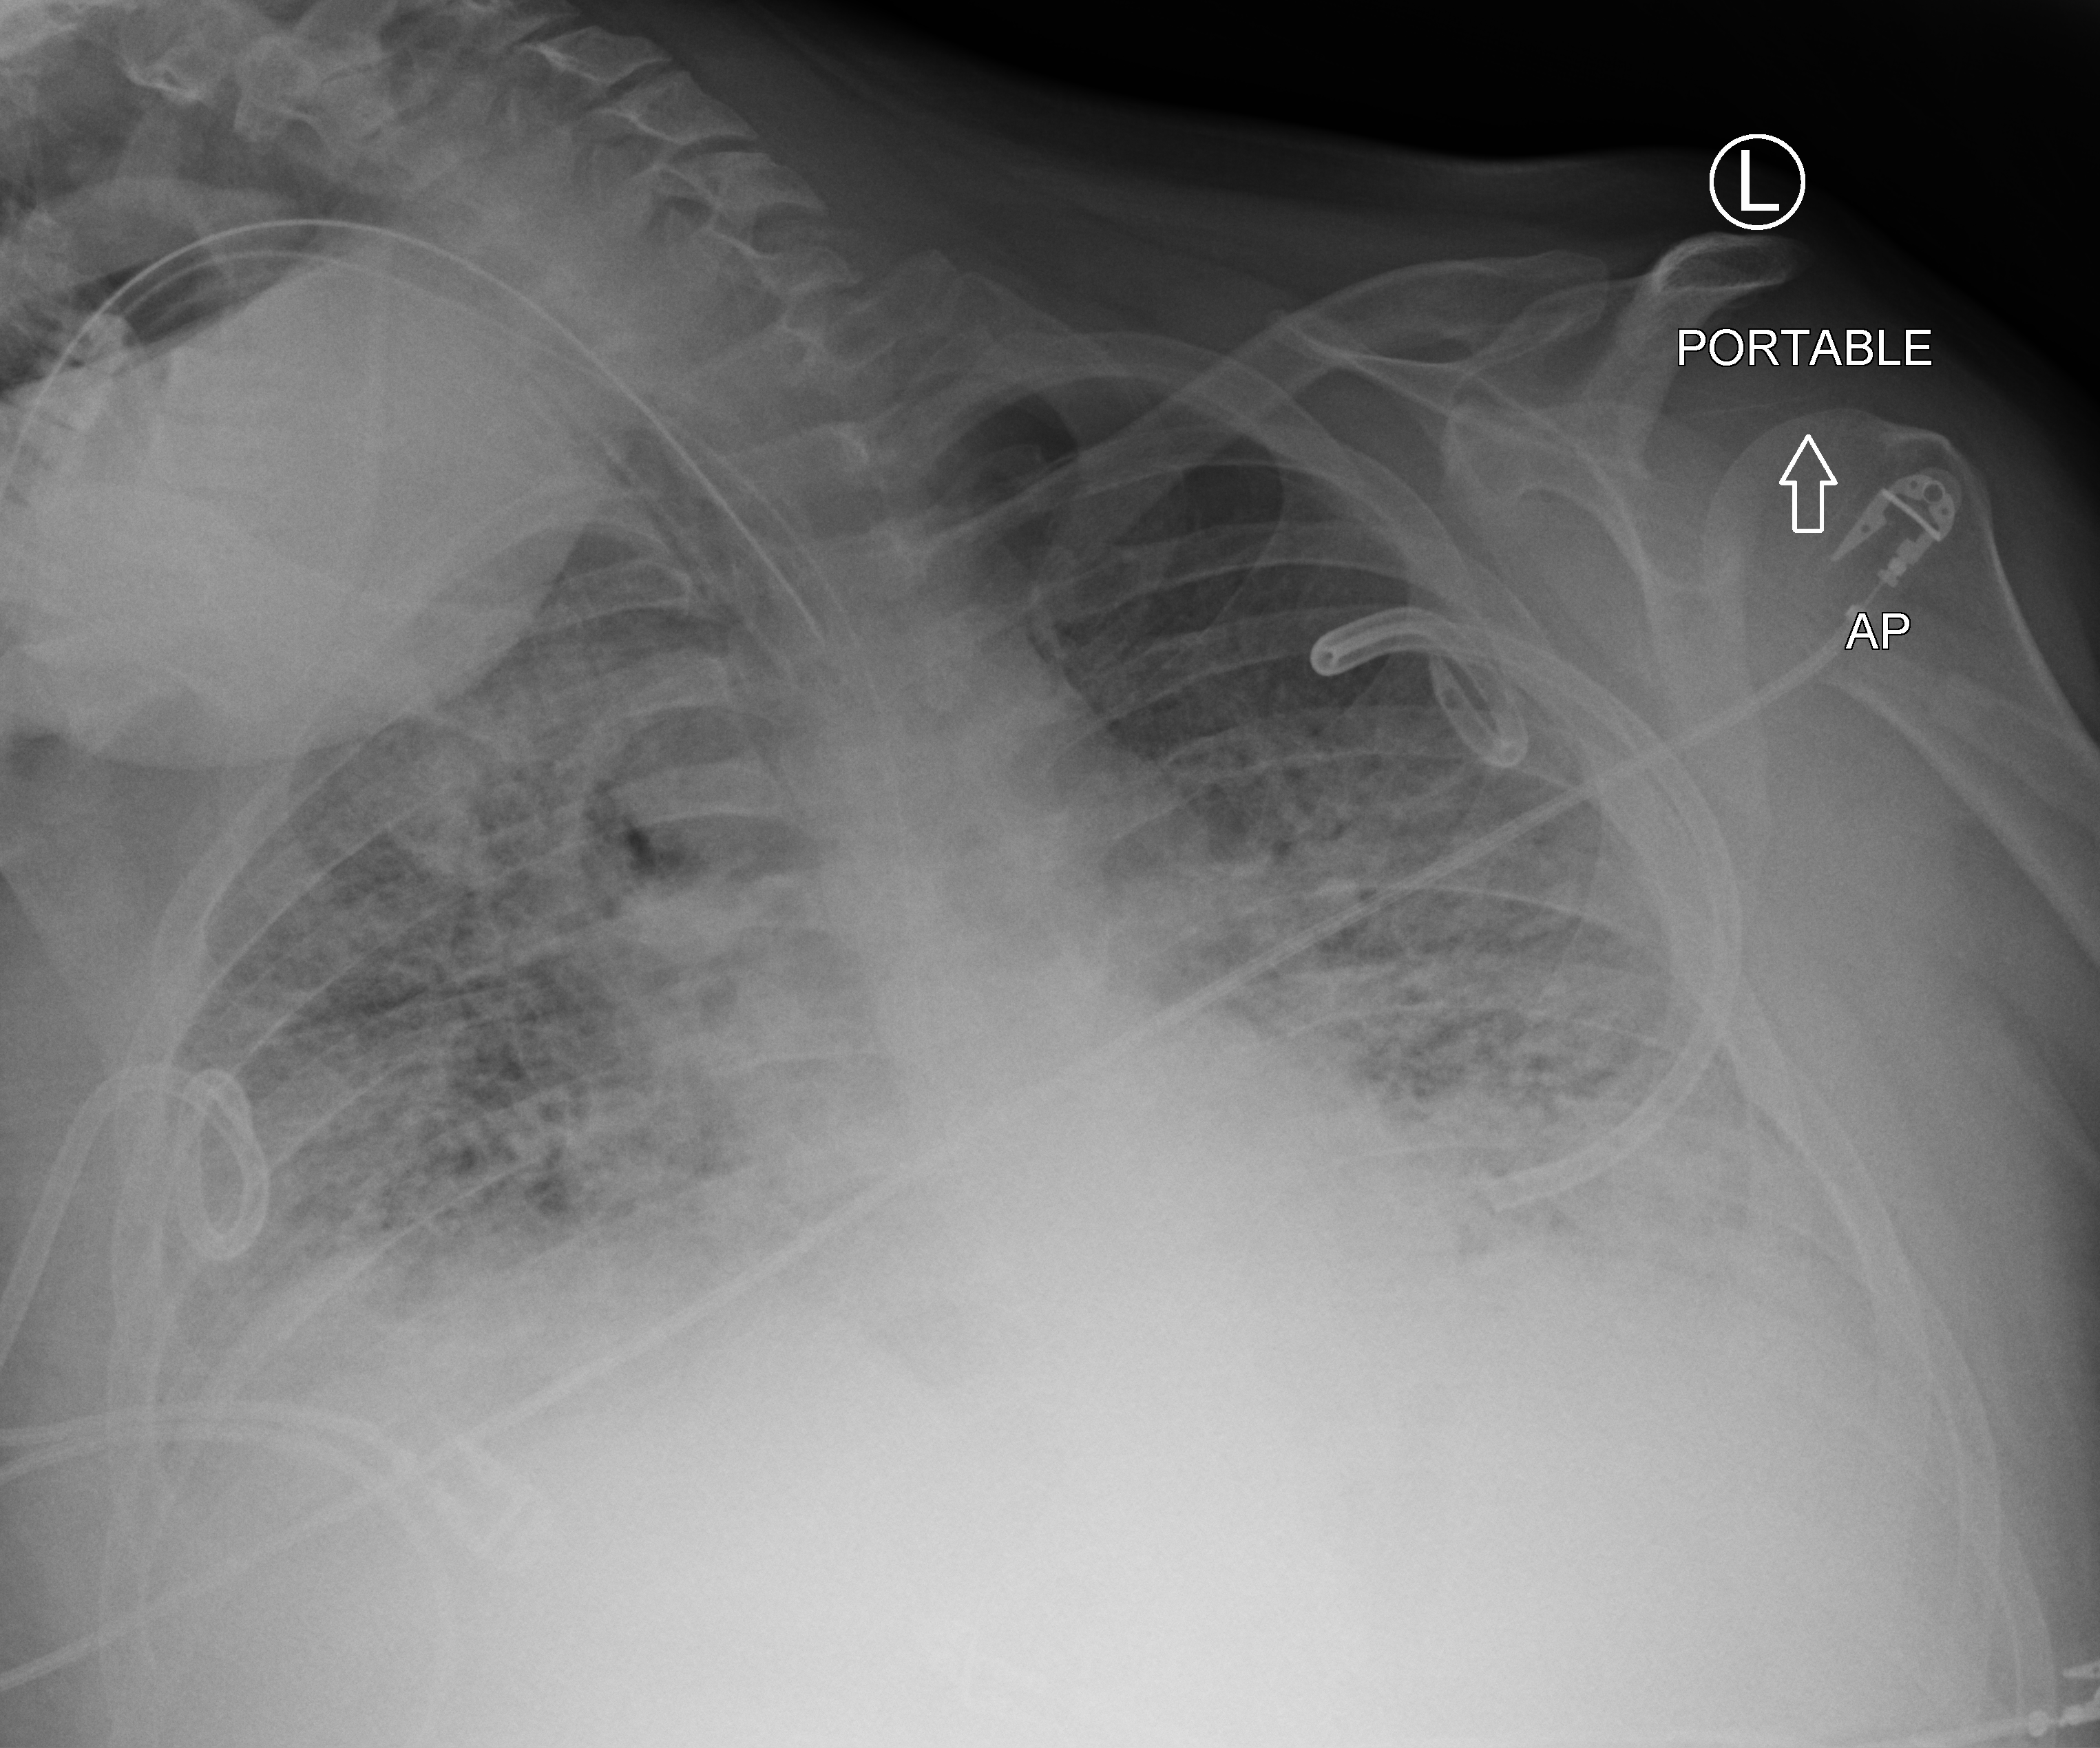
Chest X-ray (portable); anteroposterior (AP) projection. Adult patient hospitalised with COVID-19, age 18–59 years.
From the hospital-stay record, not from the radiograph (when in the stay this image was taken is not recorded): admitted to intensive care during this hospital stay: yes; length of hospital stay: 31 days; mechanically ventilated during this hospital stay: yes.